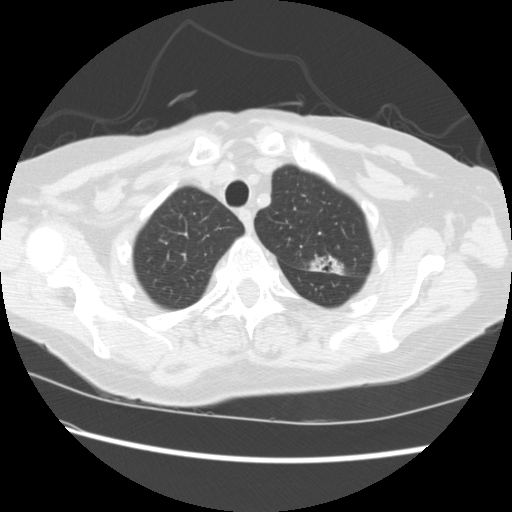
Axial slice from a low-dose chest CT screening exam, baseline annual screen, lung window (W 1500 / L -600 HU), 120 kVp, 512 × 512 image matrix, field of view 340 × 340 mm. Female, age 74 years at enrolment. Former smoker at enrolment.
Expert reader's lesion annotation, bounding box (x1, y1, x2, y2) in pixels: (297, 246, 347, 284). The screening reader recorded 2 non-calcified nodules or masses ≥4 mm on this exam (left upper lobe, right lower lobe); which of them this box marks is not recorded. Official screen result: positive, change unspecified: nodule(s) >= 4 mm or enlarging nodule(s), mass(es), or other non-specific abnormalities suspicious for lung cancer.